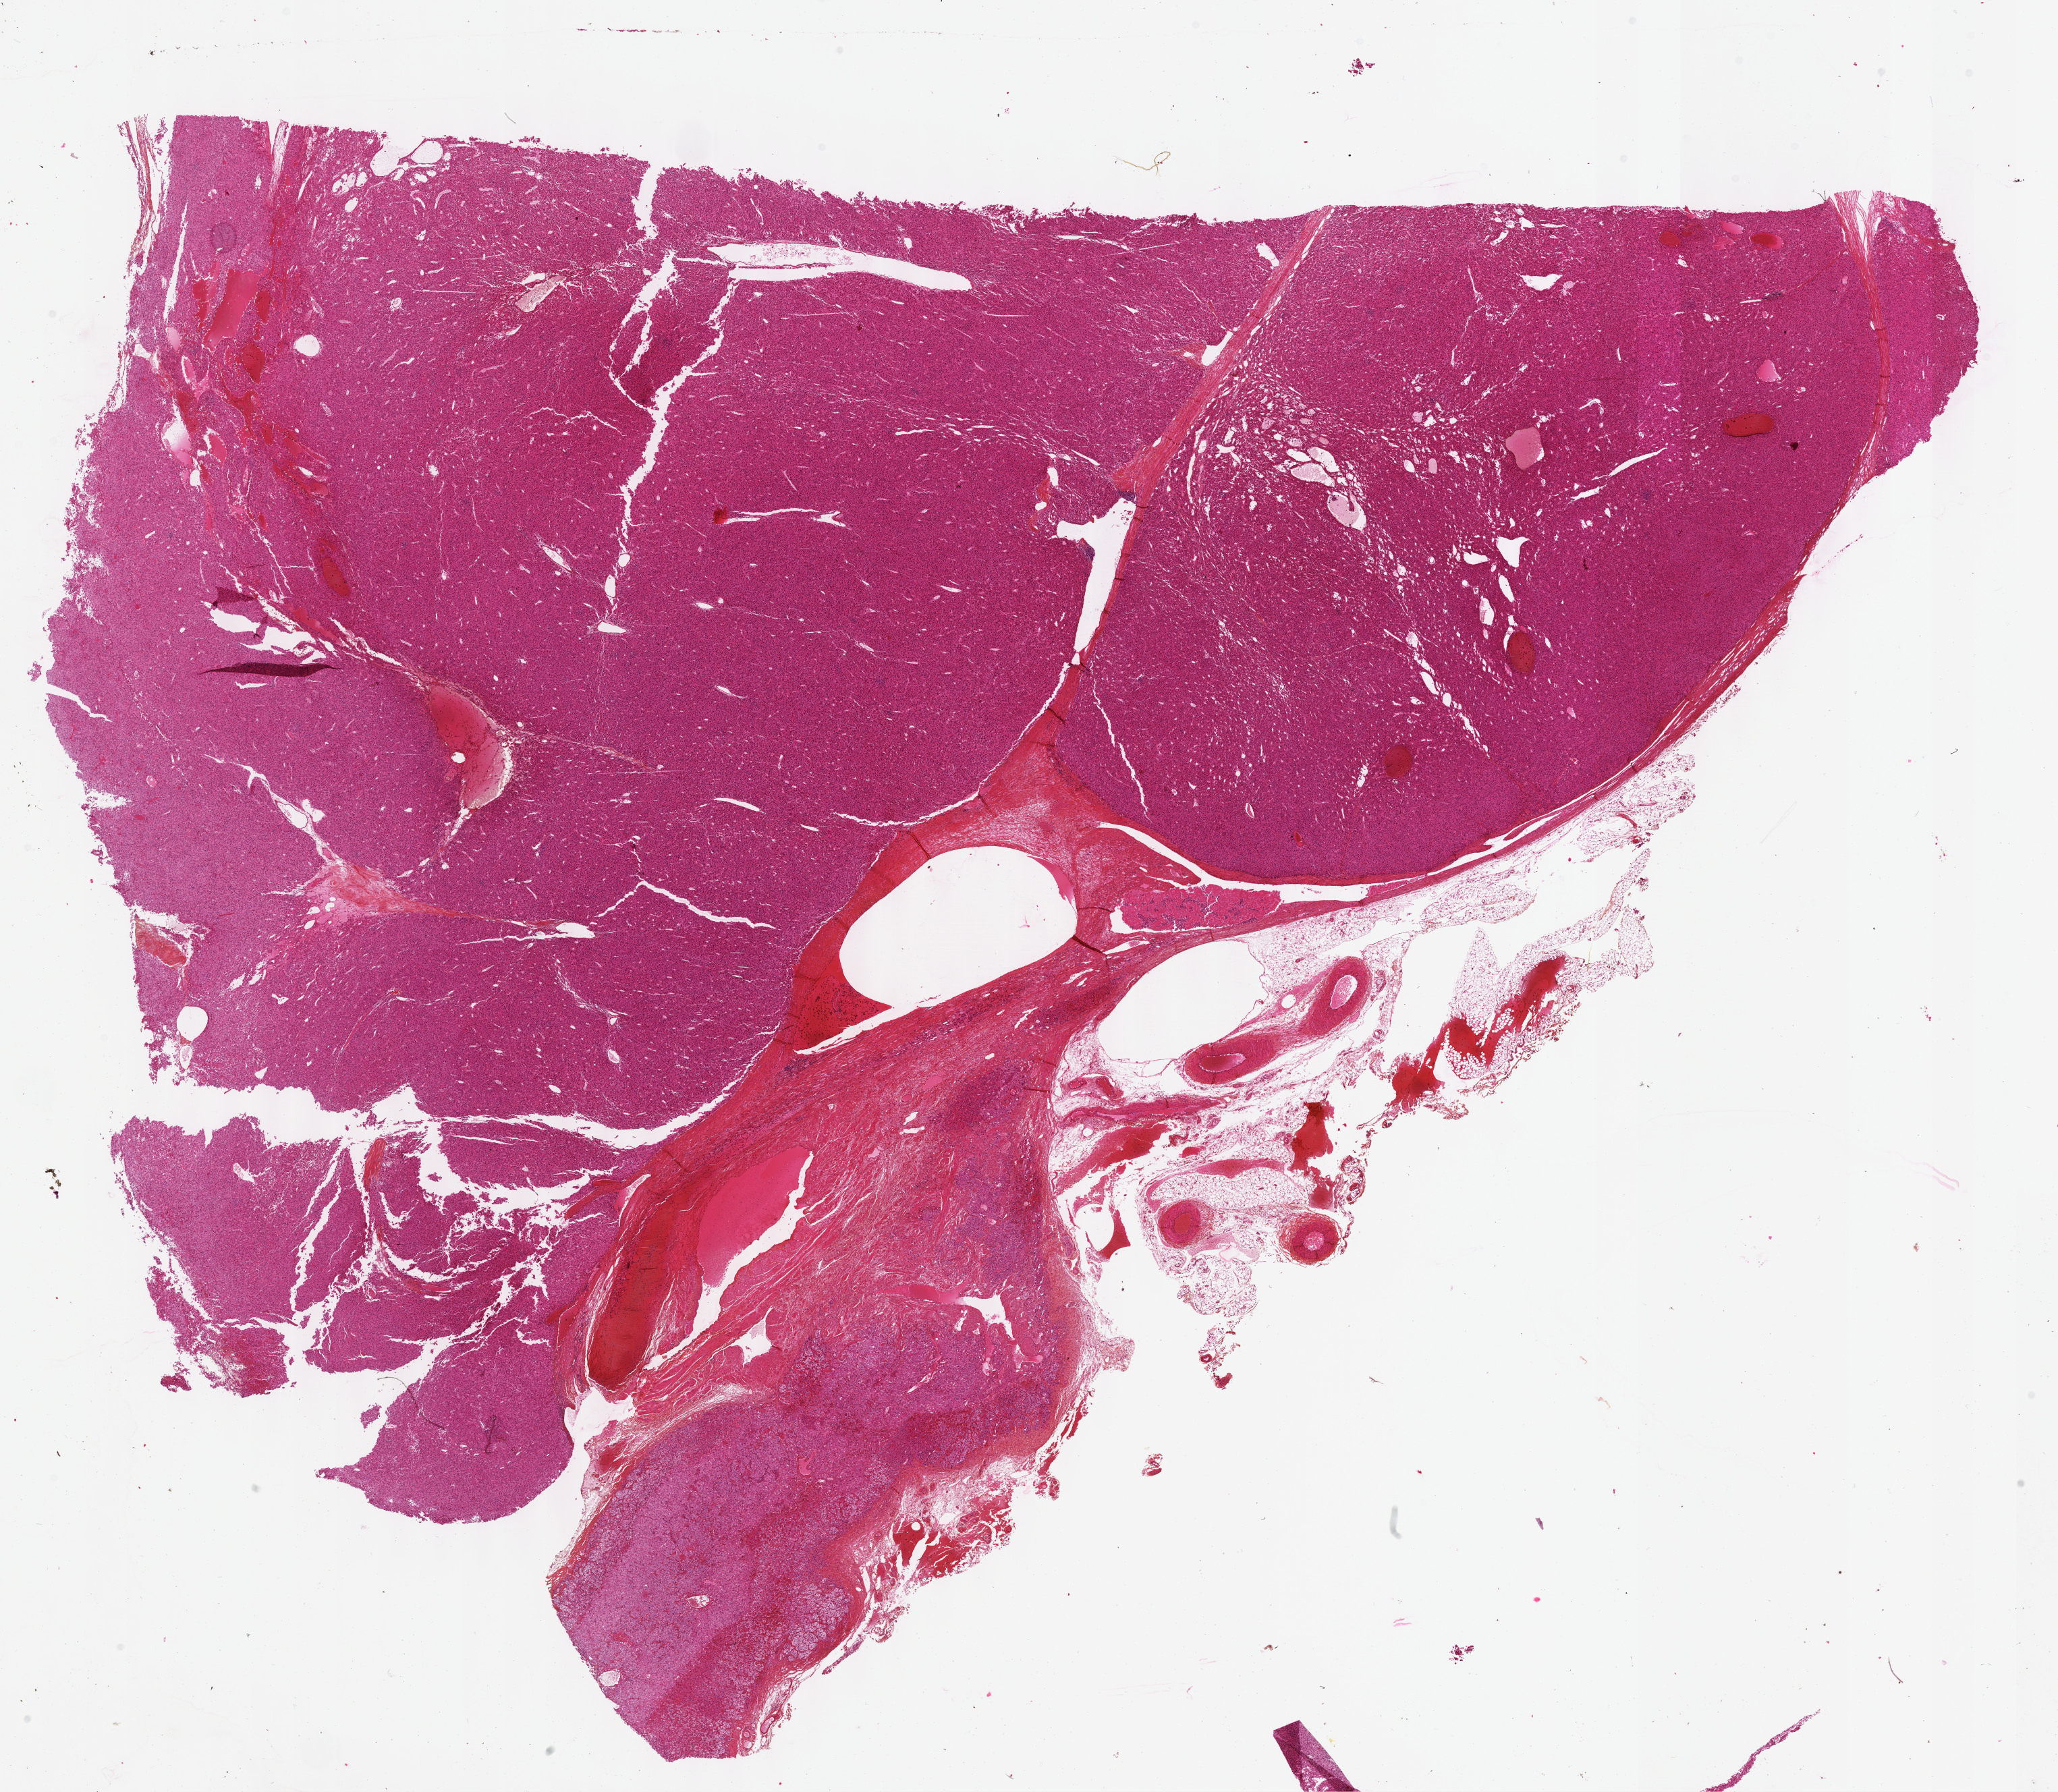
Whole-slide histology image, H&E-stained, shown as a low-resolution overview of the whole scanned area (about 24.6 x 21.5 mm, from a 40x scan). Formalin-fixed paraffin-embedded (FFPE) diagnostic section. Sample: primary tumour, adrenal cortex. Male patient; age at initial diagnosis 62 years.
Histologic diagnosis: Adrenal cortical carcinoma (cortex of adrenal gland). Laterality: right.